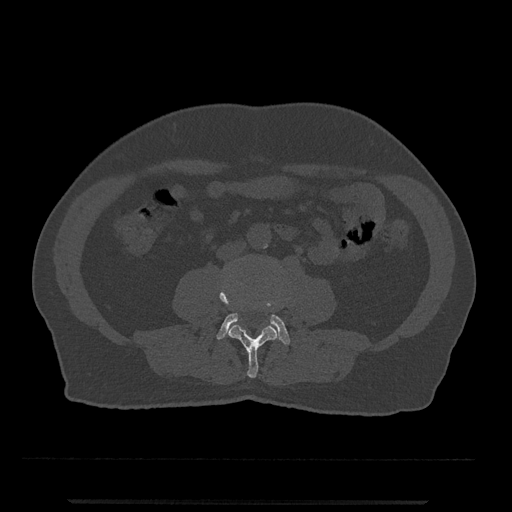
CT including the spine, one axial slice. Position 173 of 797 along the scan axis. Reconstruction kernel Br40s/3. Bone window (W 1800 / L 400 HU). 0.5 mm slice thickness. 512 × 512 image matrix. Patient: male, 63 years. Case-level facts recorded for this patient, not image findings: primary cancer: prostate.
Annotated regions visible in this slice (semi-automatic segmentation, software-assisted and operator-edited):
- L3 vertebra: bounding box (x1, y1, x2, y2) in pixels: (219, 291, 277, 378)
- L4 vertebra: (217, 302, 290, 345)